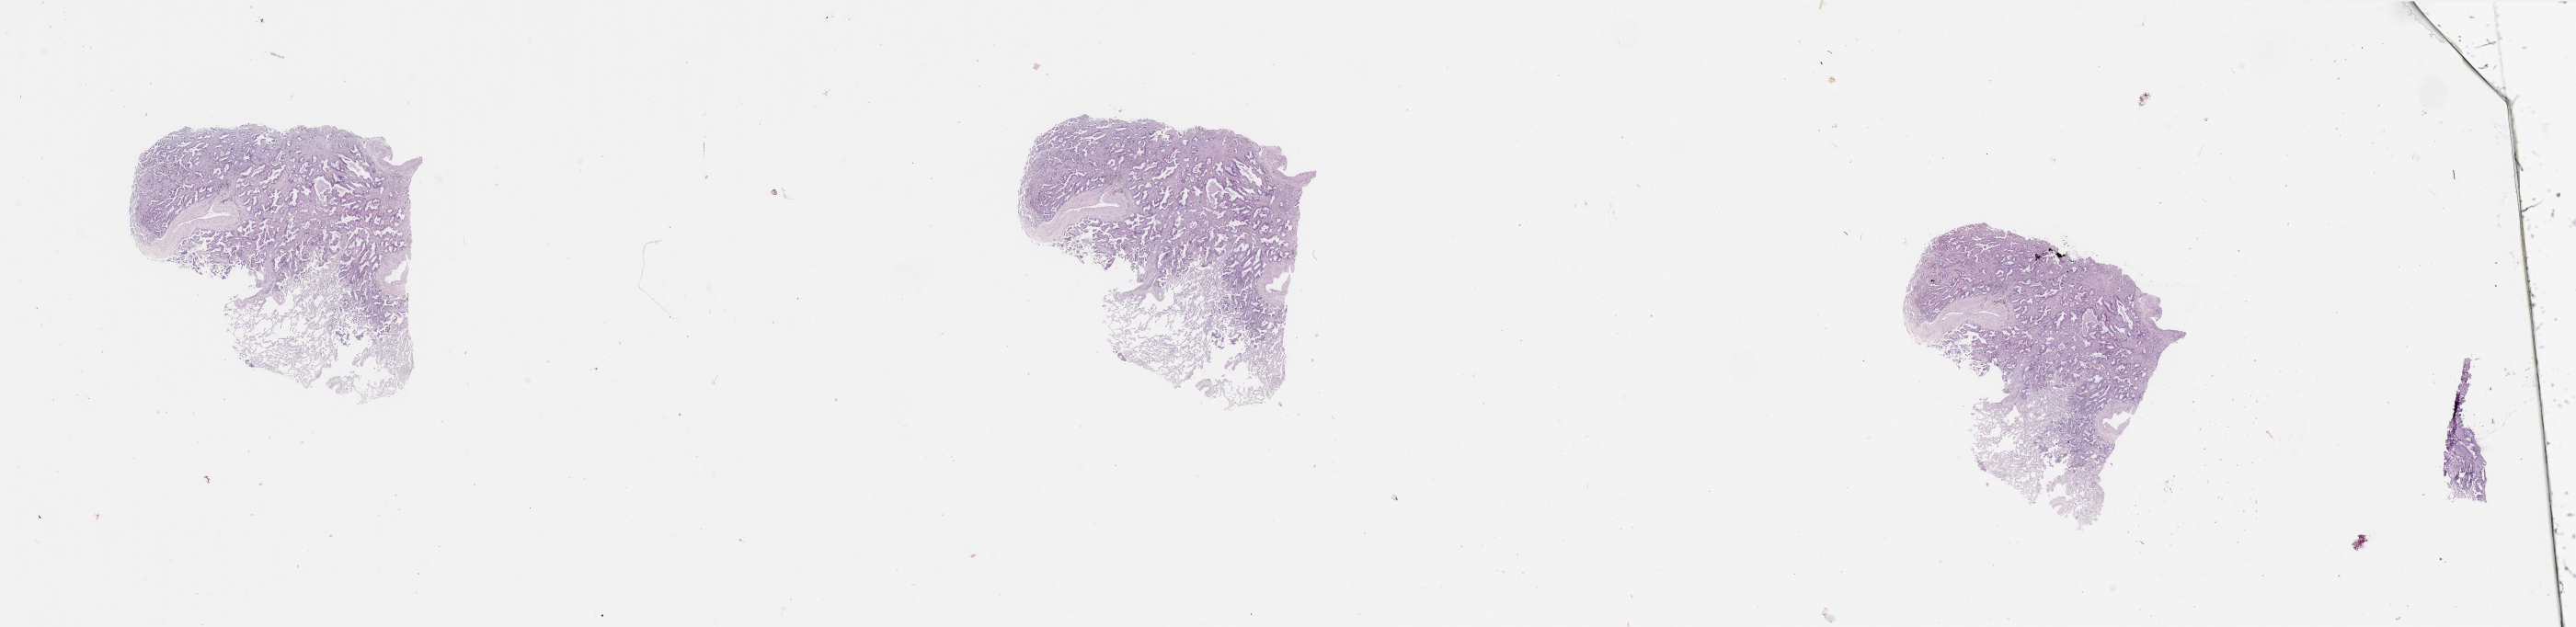
H&E-stained whole-slide image — whole scanned area (about 44.3 x 10.8 mm, from a 20x scan) shown as a low-resolution overview. Tumour tissue sample, sampled site: lung. Patient: male, age 77 years. Histologic grade: G2 (moderately differentiated). Composition of this section per pathologist review: tumour nuclei 70%, necrosis 0%.
Diagnosis: Adenocarcinoma, NOS. AJCC pathologic stage: IIIA.